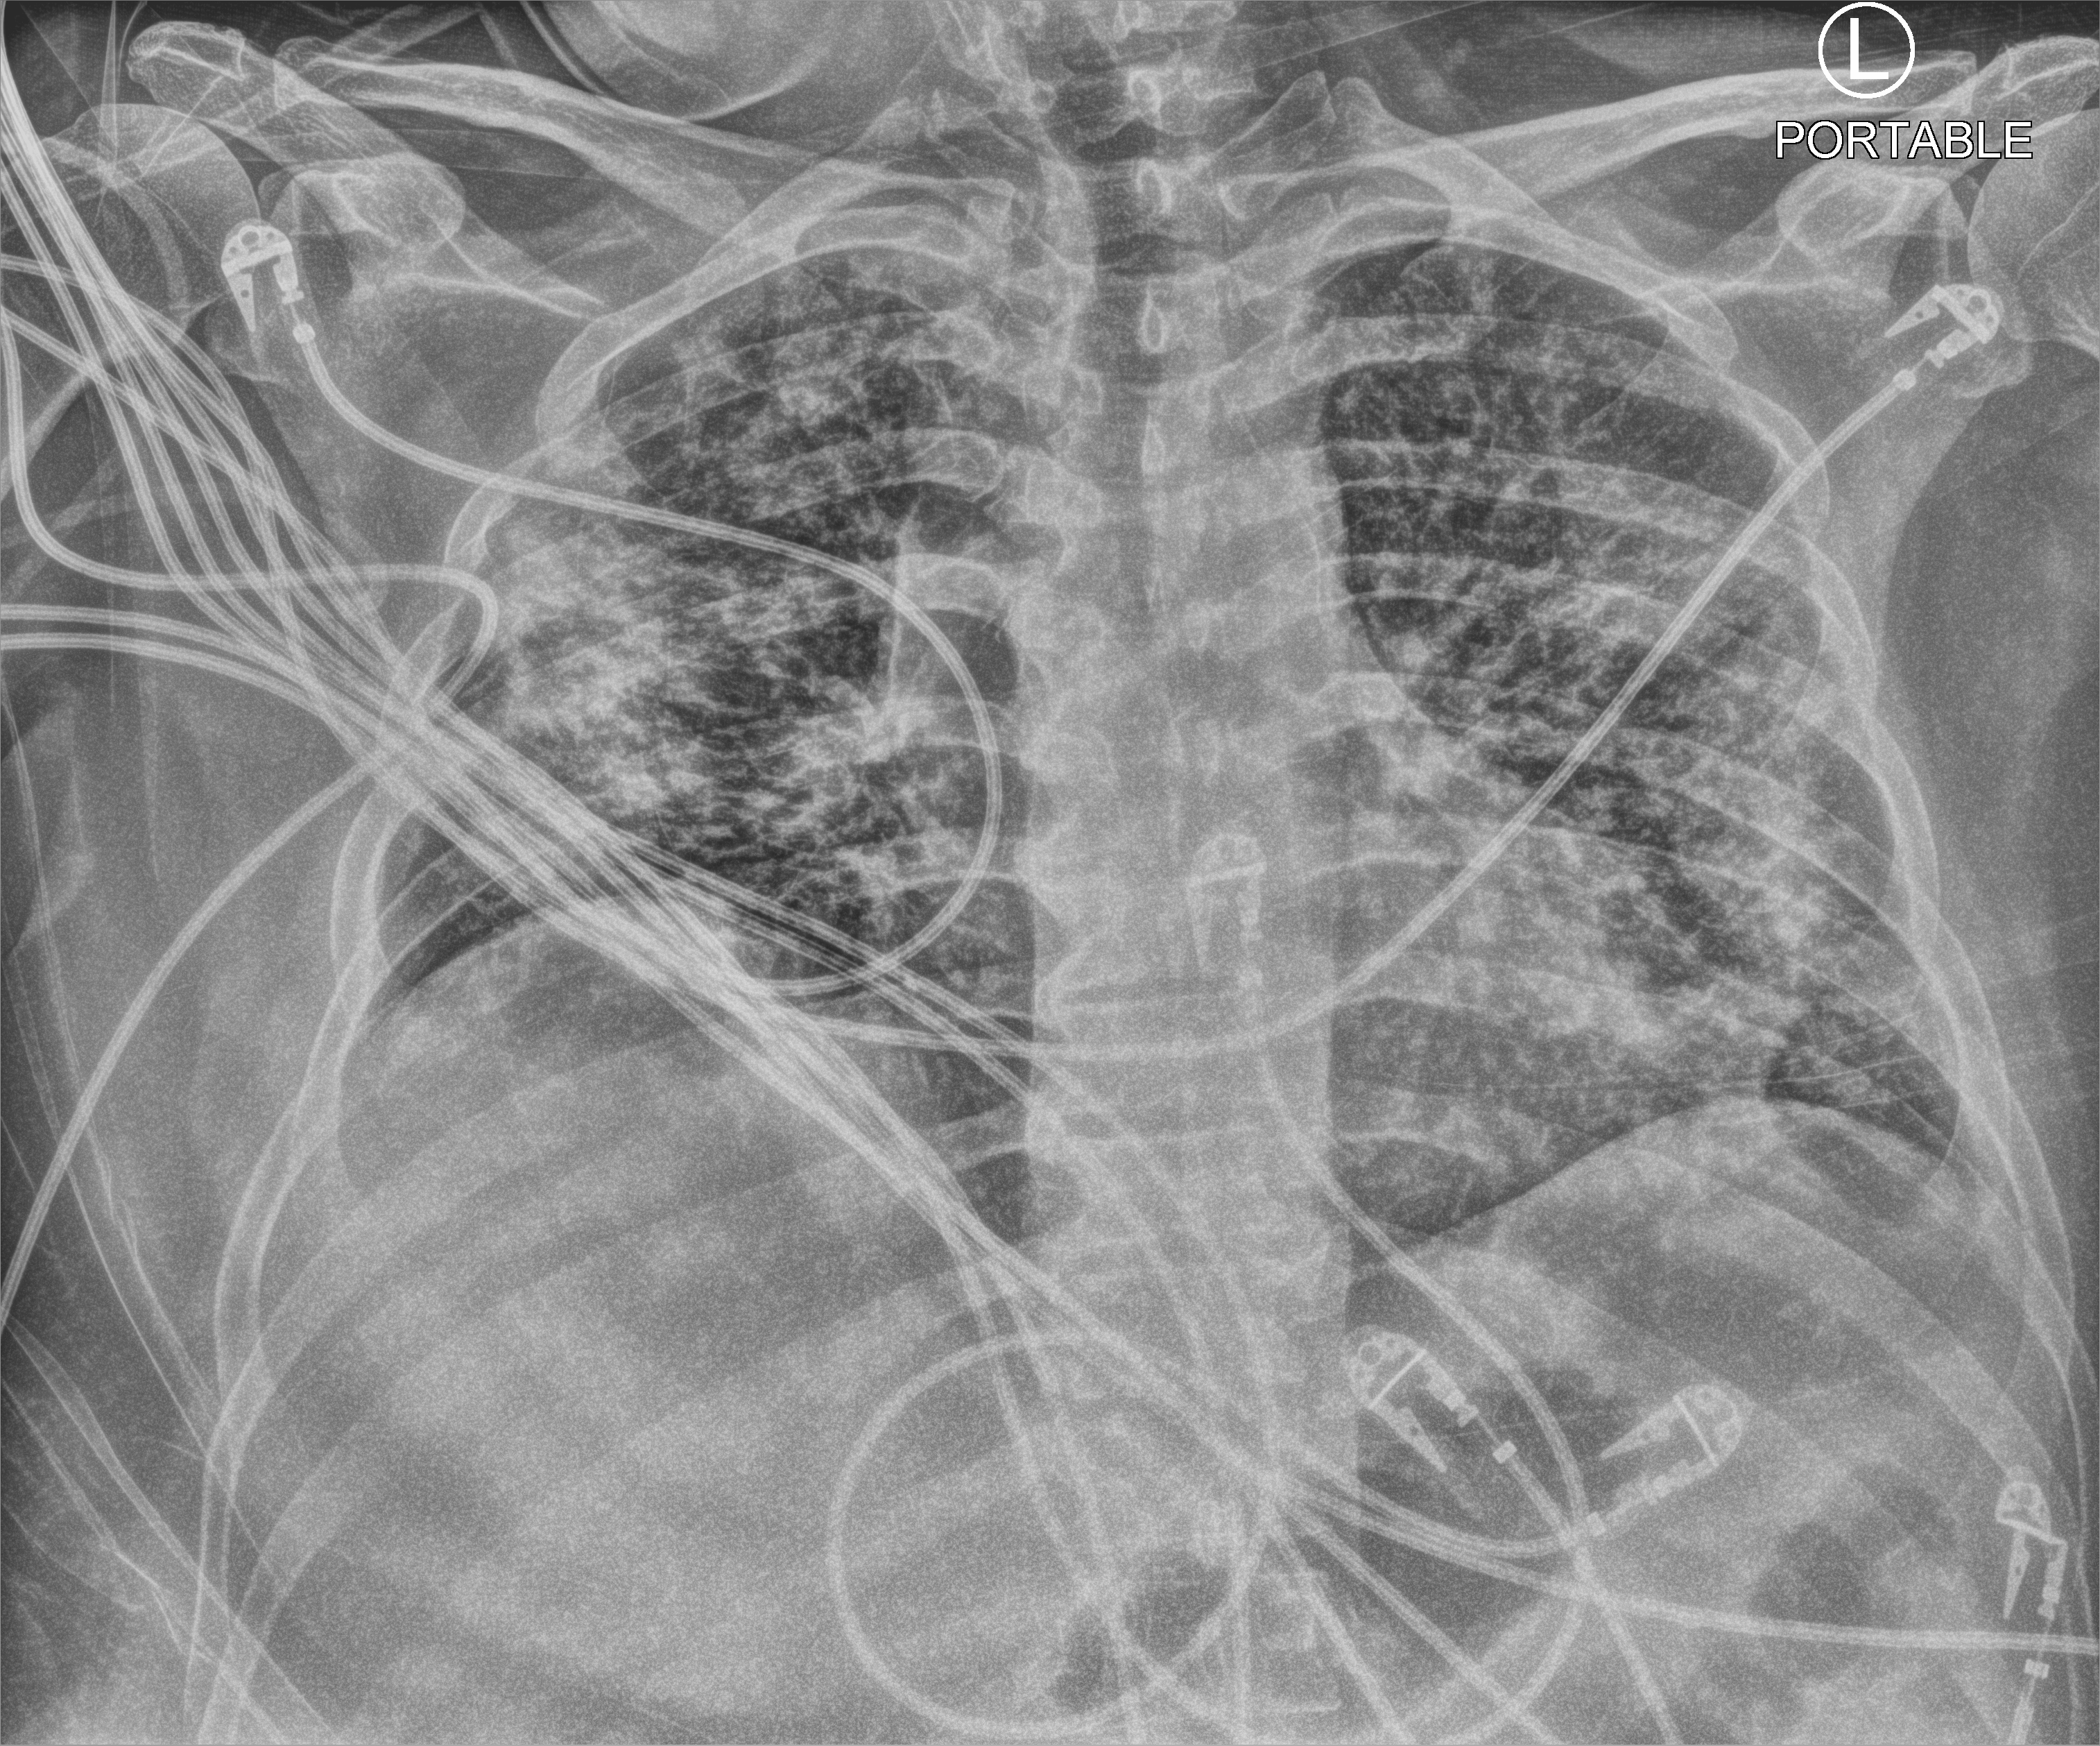
Bedside chest radiograph (computed radiography); anteroposterior (AP) projection. Male patient hospitalised with COVID-19, age 18–59 years.
Hospital-stay facts (about this admission, not read from this image; timing relative to this image not recorded): length of hospital stay: 24 days; mechanically ventilated during this hospital stay: yes; admitted to intensive care during this hospital stay: yes.